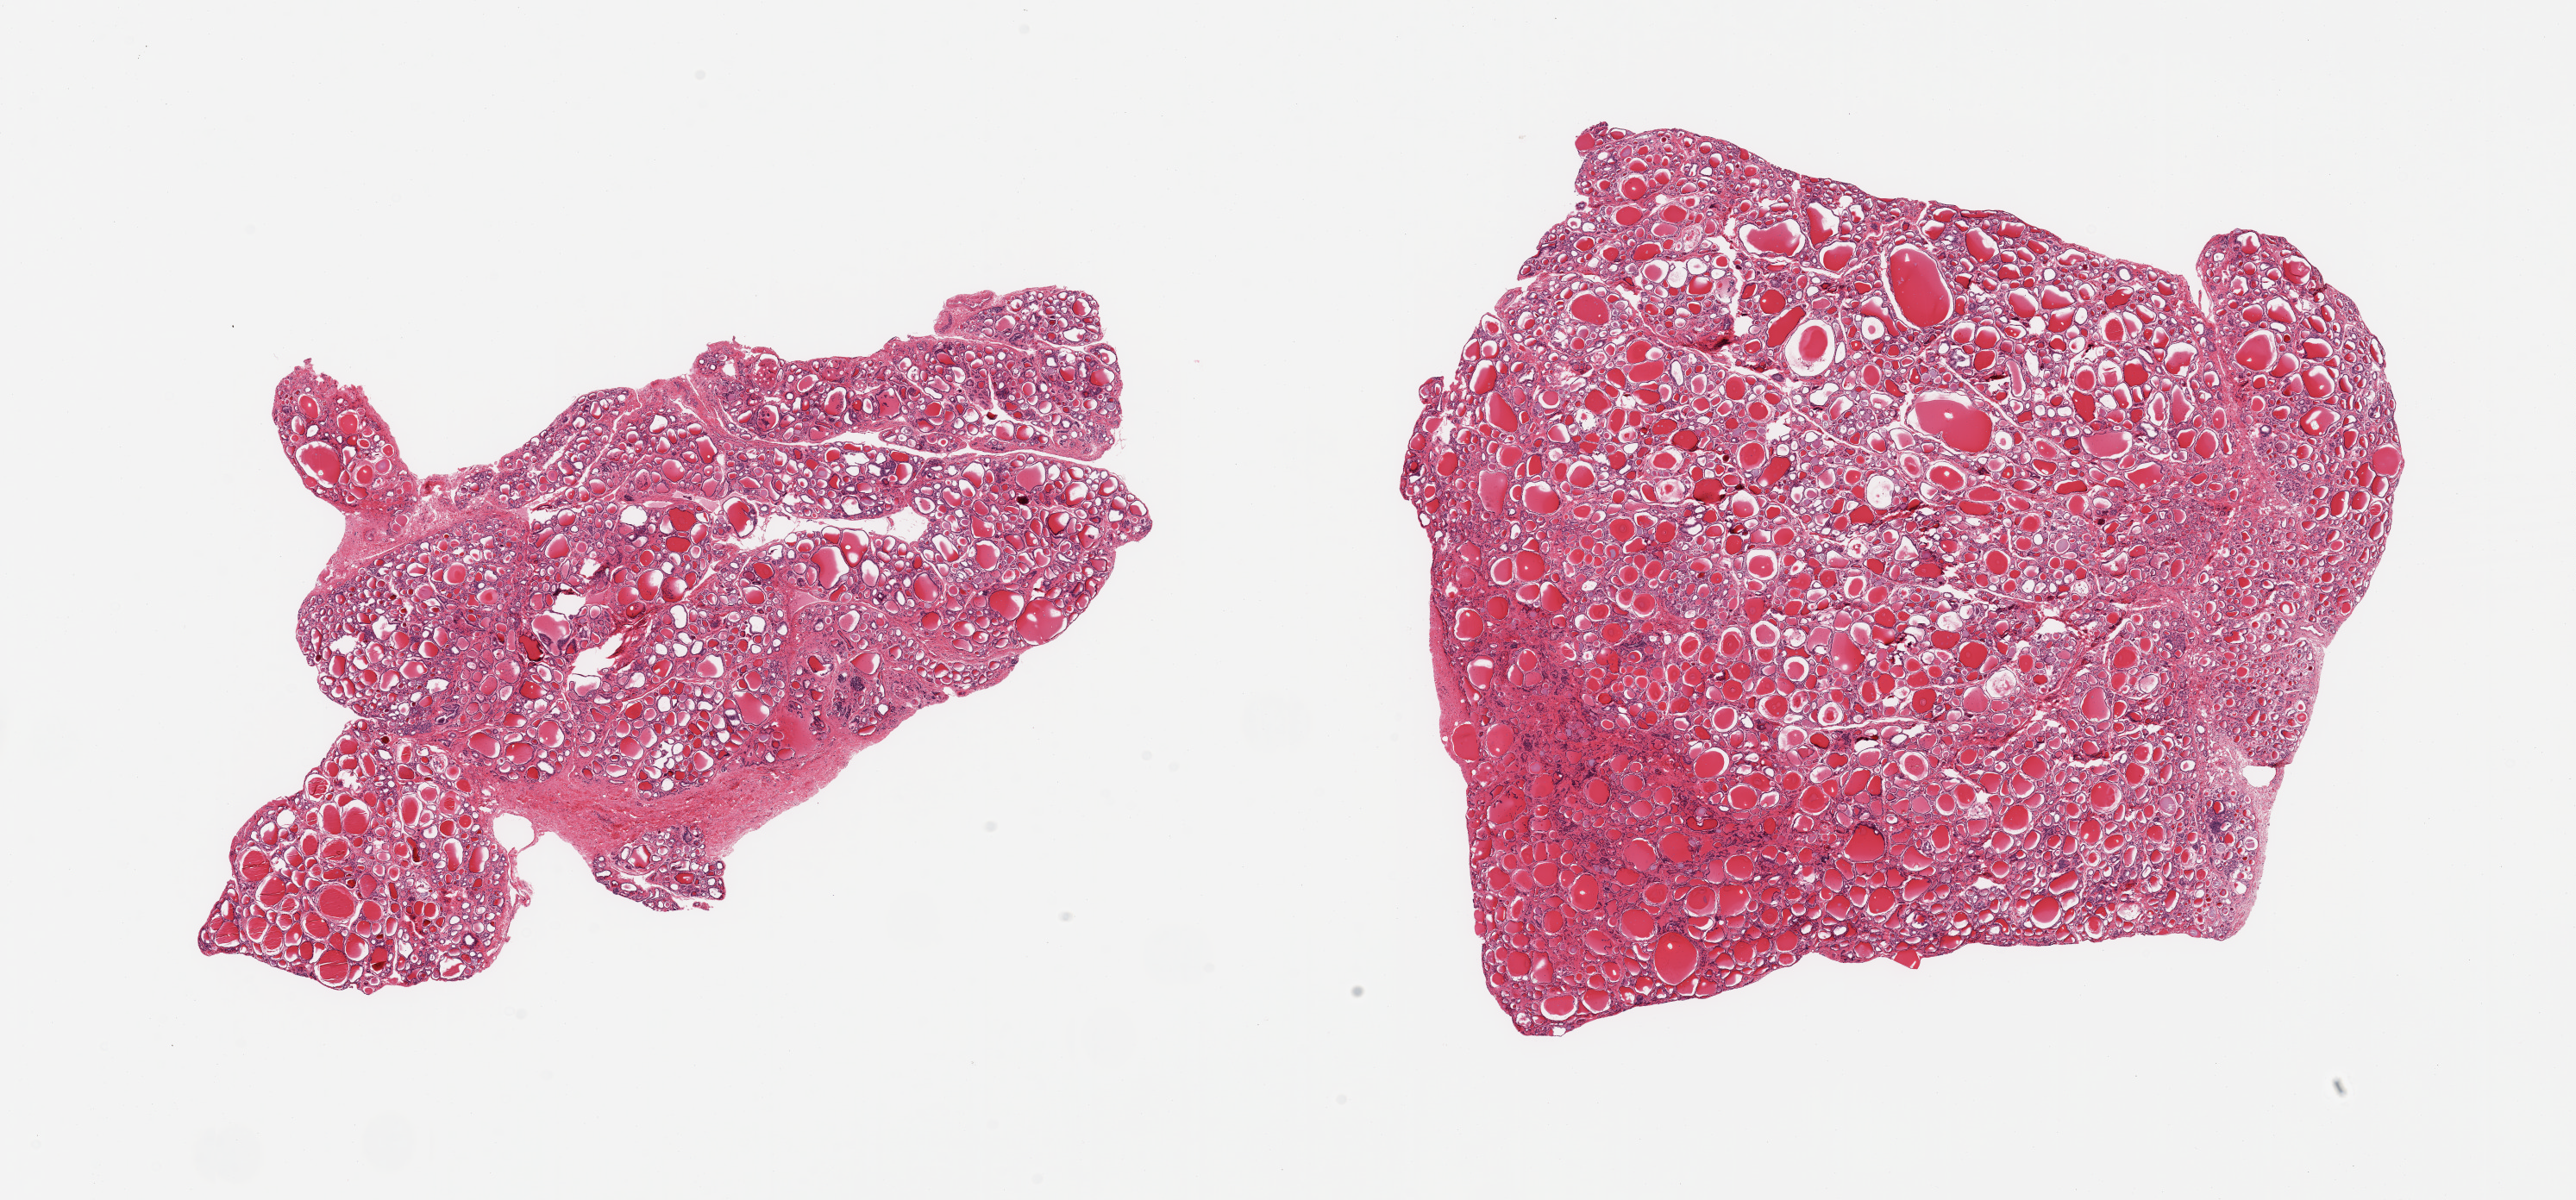
Whole-slide image, haematoxylin and eosin stain, brightfield, whole scanned area (about 23.6 x 11.0 mm, from a 20x scan) shown as a low-resolution overview. PAXgene-fixed paraffin-embedded (PFPE) section. Sampled site (target tissue): thyroid. Tissue donor sample. Donor sex: male.
Review note (as recorded): 2 pieces; no lesions.